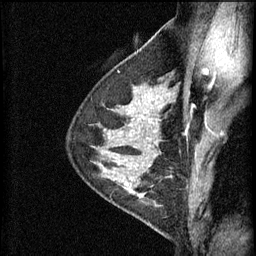
Breast MRI (dynamic contrast-enhanced), one sagittal slice; position 41 of 60 along the scan axis; 3 images stored at this slice position (order not interpretable as contrast timing); 1.5 T; TE 4.2 ms, TR 11 ms; 2 mm slice thickness; 256 × 256 image matrix, field of view 180 × 180 mm. Patient: female, 29 years.
Structures marked on this image (semi-automatically segmented with operator editing):
- analysis volume of interest (the breast-tissue region the enhancement analysis was run in; not a lesion): bounding box (x1, y1, x2, y2) in pixels: (105, 172, 169, 227)
- tumour enhancement mask (voxels above the 70 % enhancement threshold inside the analysis volume of interest): (114, 172, 147, 197)